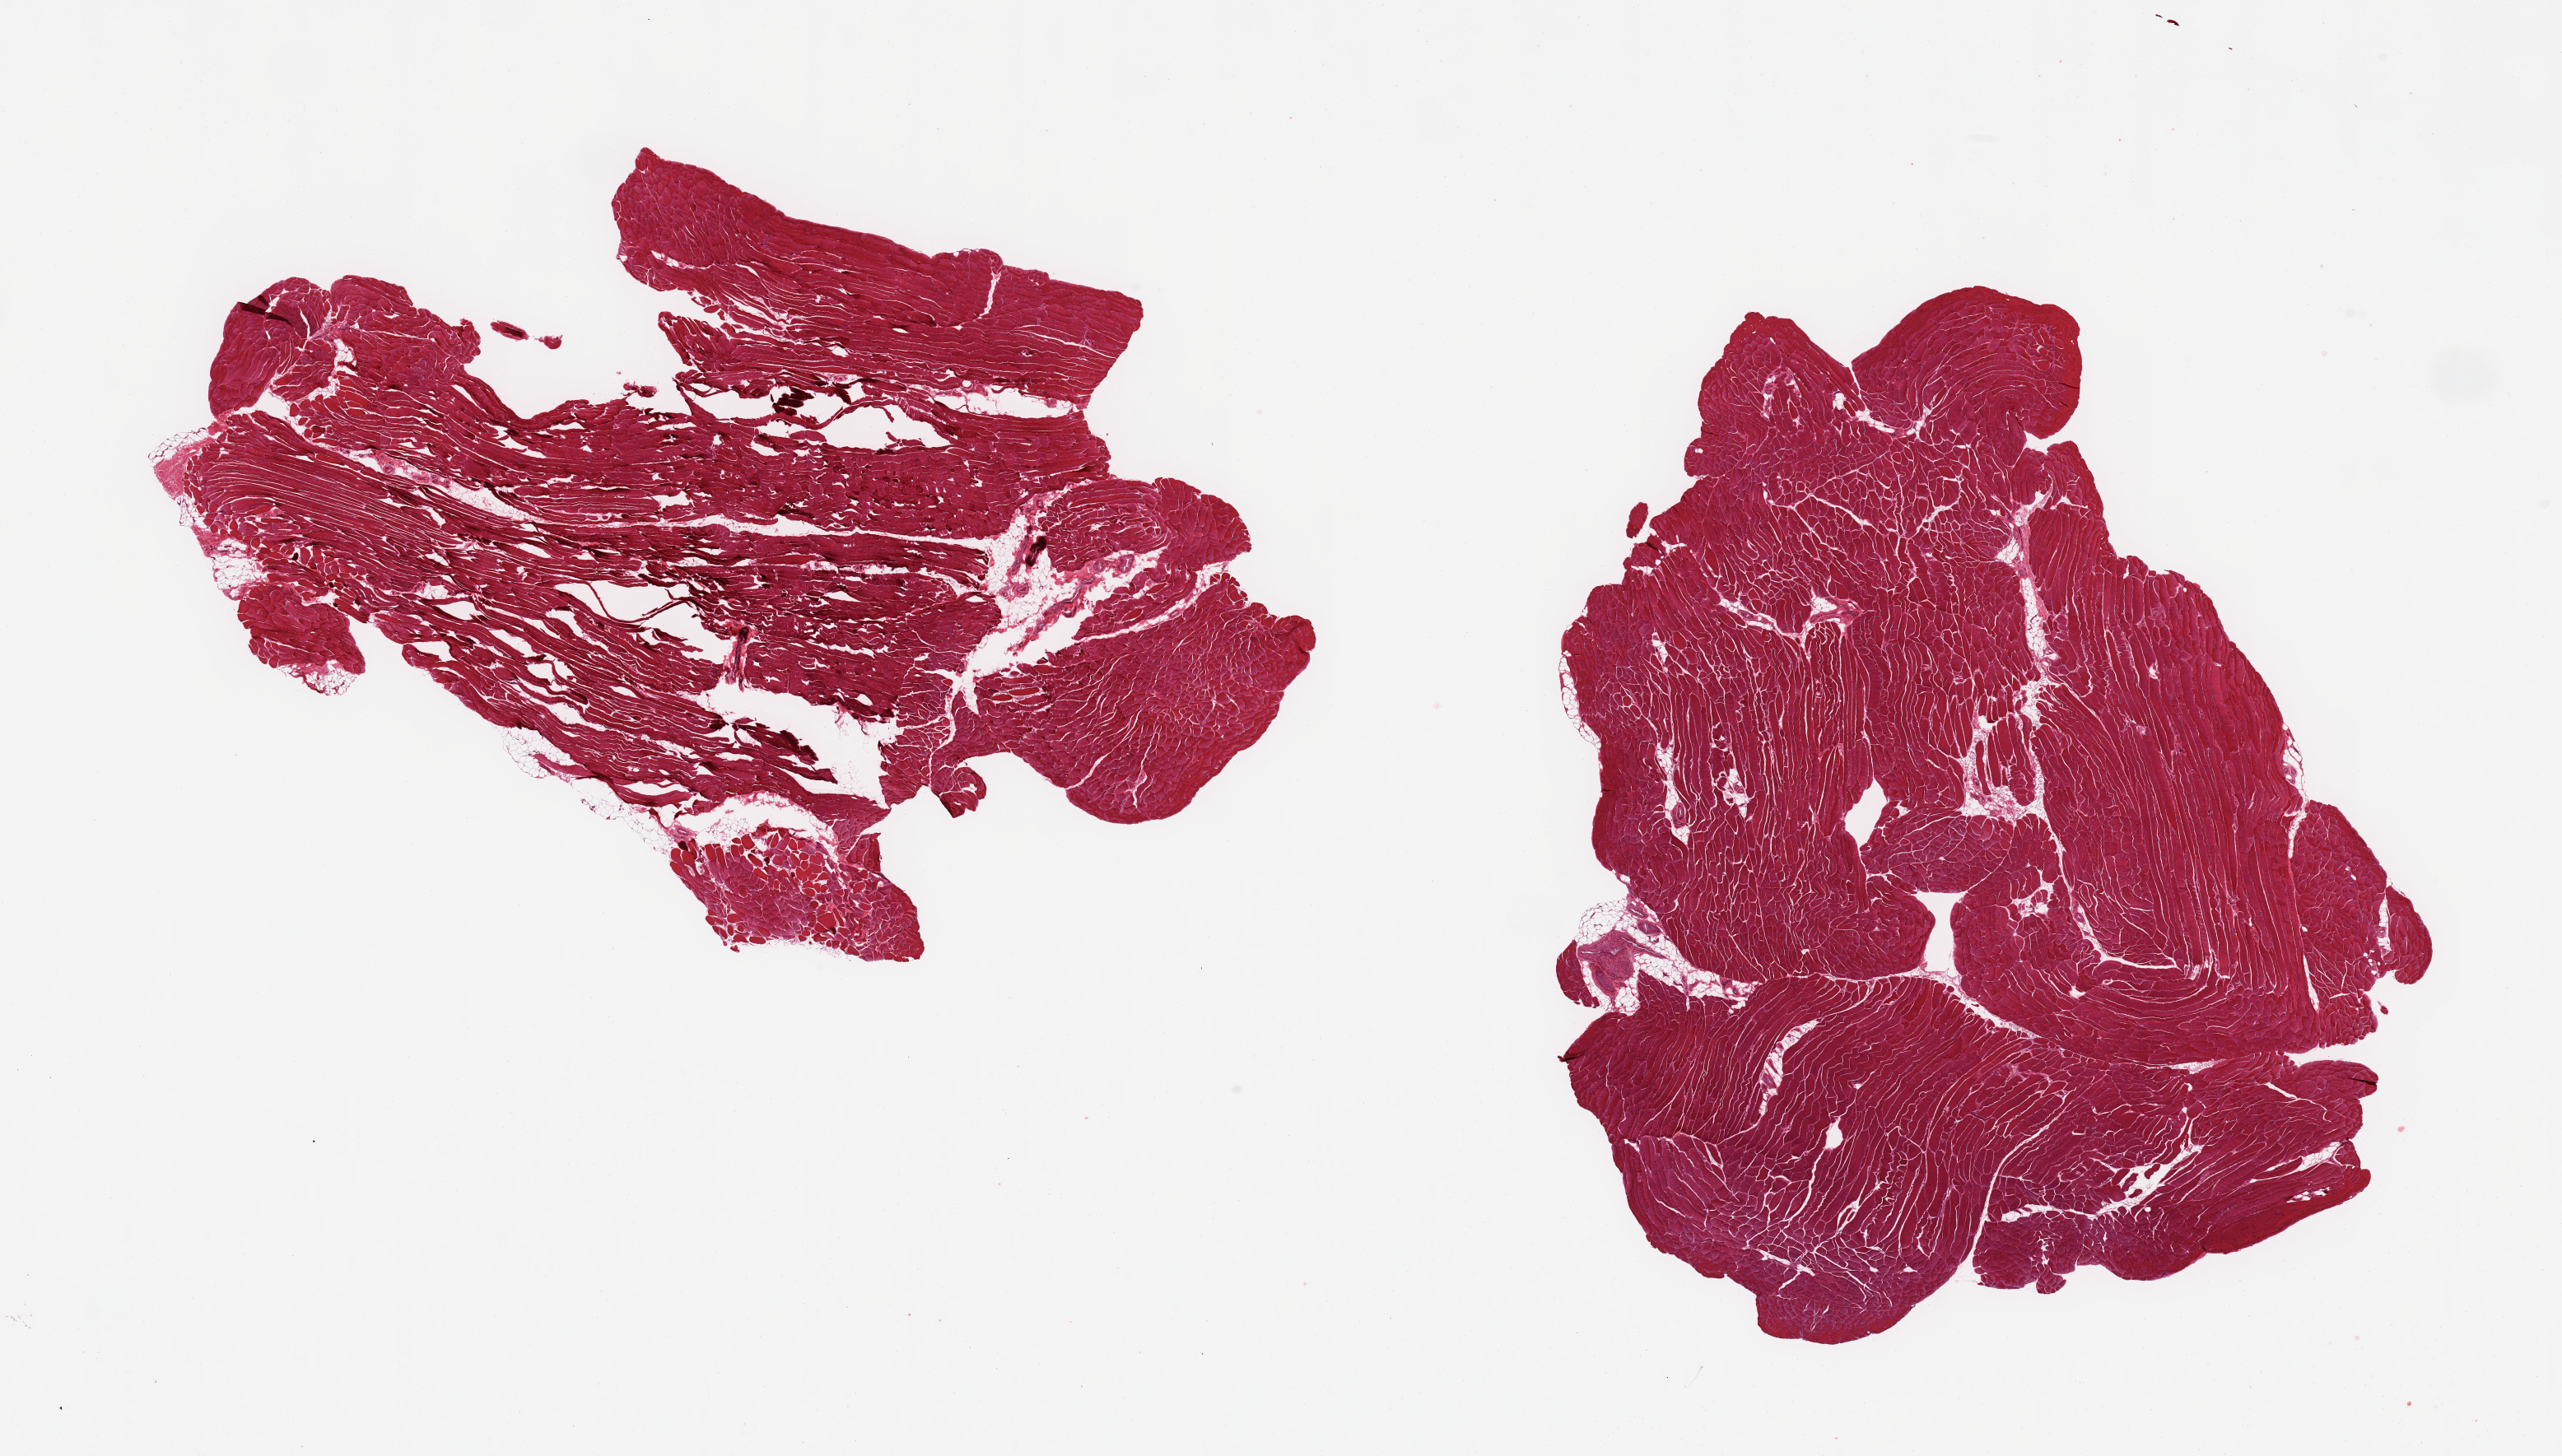
Whole-slide image, H&E stain, brightfield — a low-resolution overview of the entire scanned area, about 24.6 x 14.0 mm (acquisition: 20x scan), PAXgene-fixed, paraffin-embedded tissue, section of skeletal muscle (target tissue), donor tissue sample.
- pathologist's review note for this sample: 2 pieces; 5% internal fat